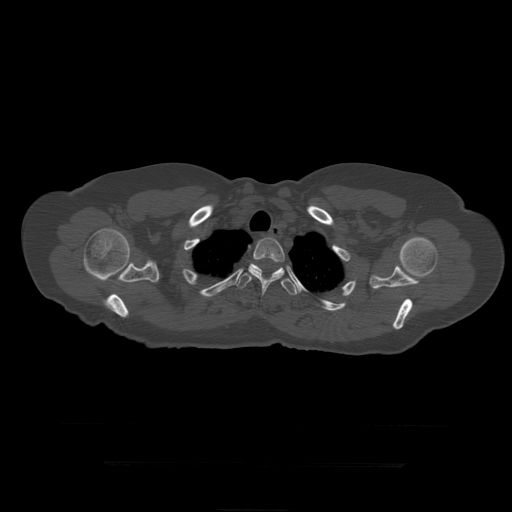
CT including the spine, one axial slice; position 358 of 399 along the scan axis; 120 kVp; bone window (W 1800 / L 400 HU); 1.25 mm slice thickness; 512 × 512 image matrix, field of view 450 × 450 mm. Patient age 41 years. Case-level facts recorded for this patient, not image findings: primary cancer: breast.
Outlined on this slice (semi-automatically segmented with operator editing):
- T3 vertebra: box from (x=248, y=238) to (x=285, y=301) px
- T4 vertebra: (x=236, y=264)–(x=299, y=296)